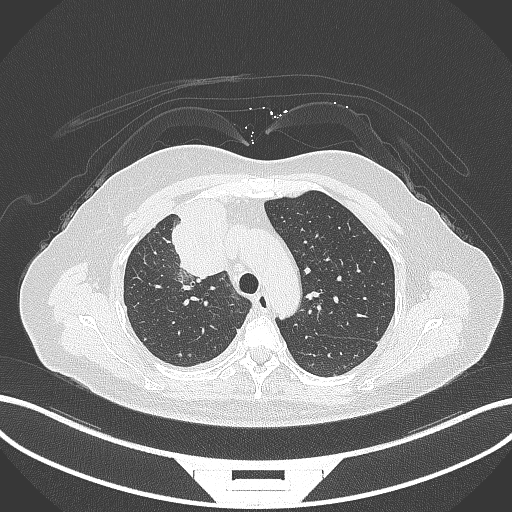
Chest CT, one axial slice. Slice 215 of 305 in the series (ordered by position). 120 kVp. Lung window (W 1500 / L -600 HU). 1 mm slice thickness. 512 × 512 image matrix, field of view 400 × 400 mm. Female patient, age 52 years. From the clinical record (not read from this slice): clinical TNM (as recorded): T3 N1 M1.
Annotated regions visible in this slice (rectangle marked by the reading radiologist):
- lung tumour (recorded histology: adenocarcinoma): bounding box <164,194,234,282> (left, top, right, bottom; pixels)